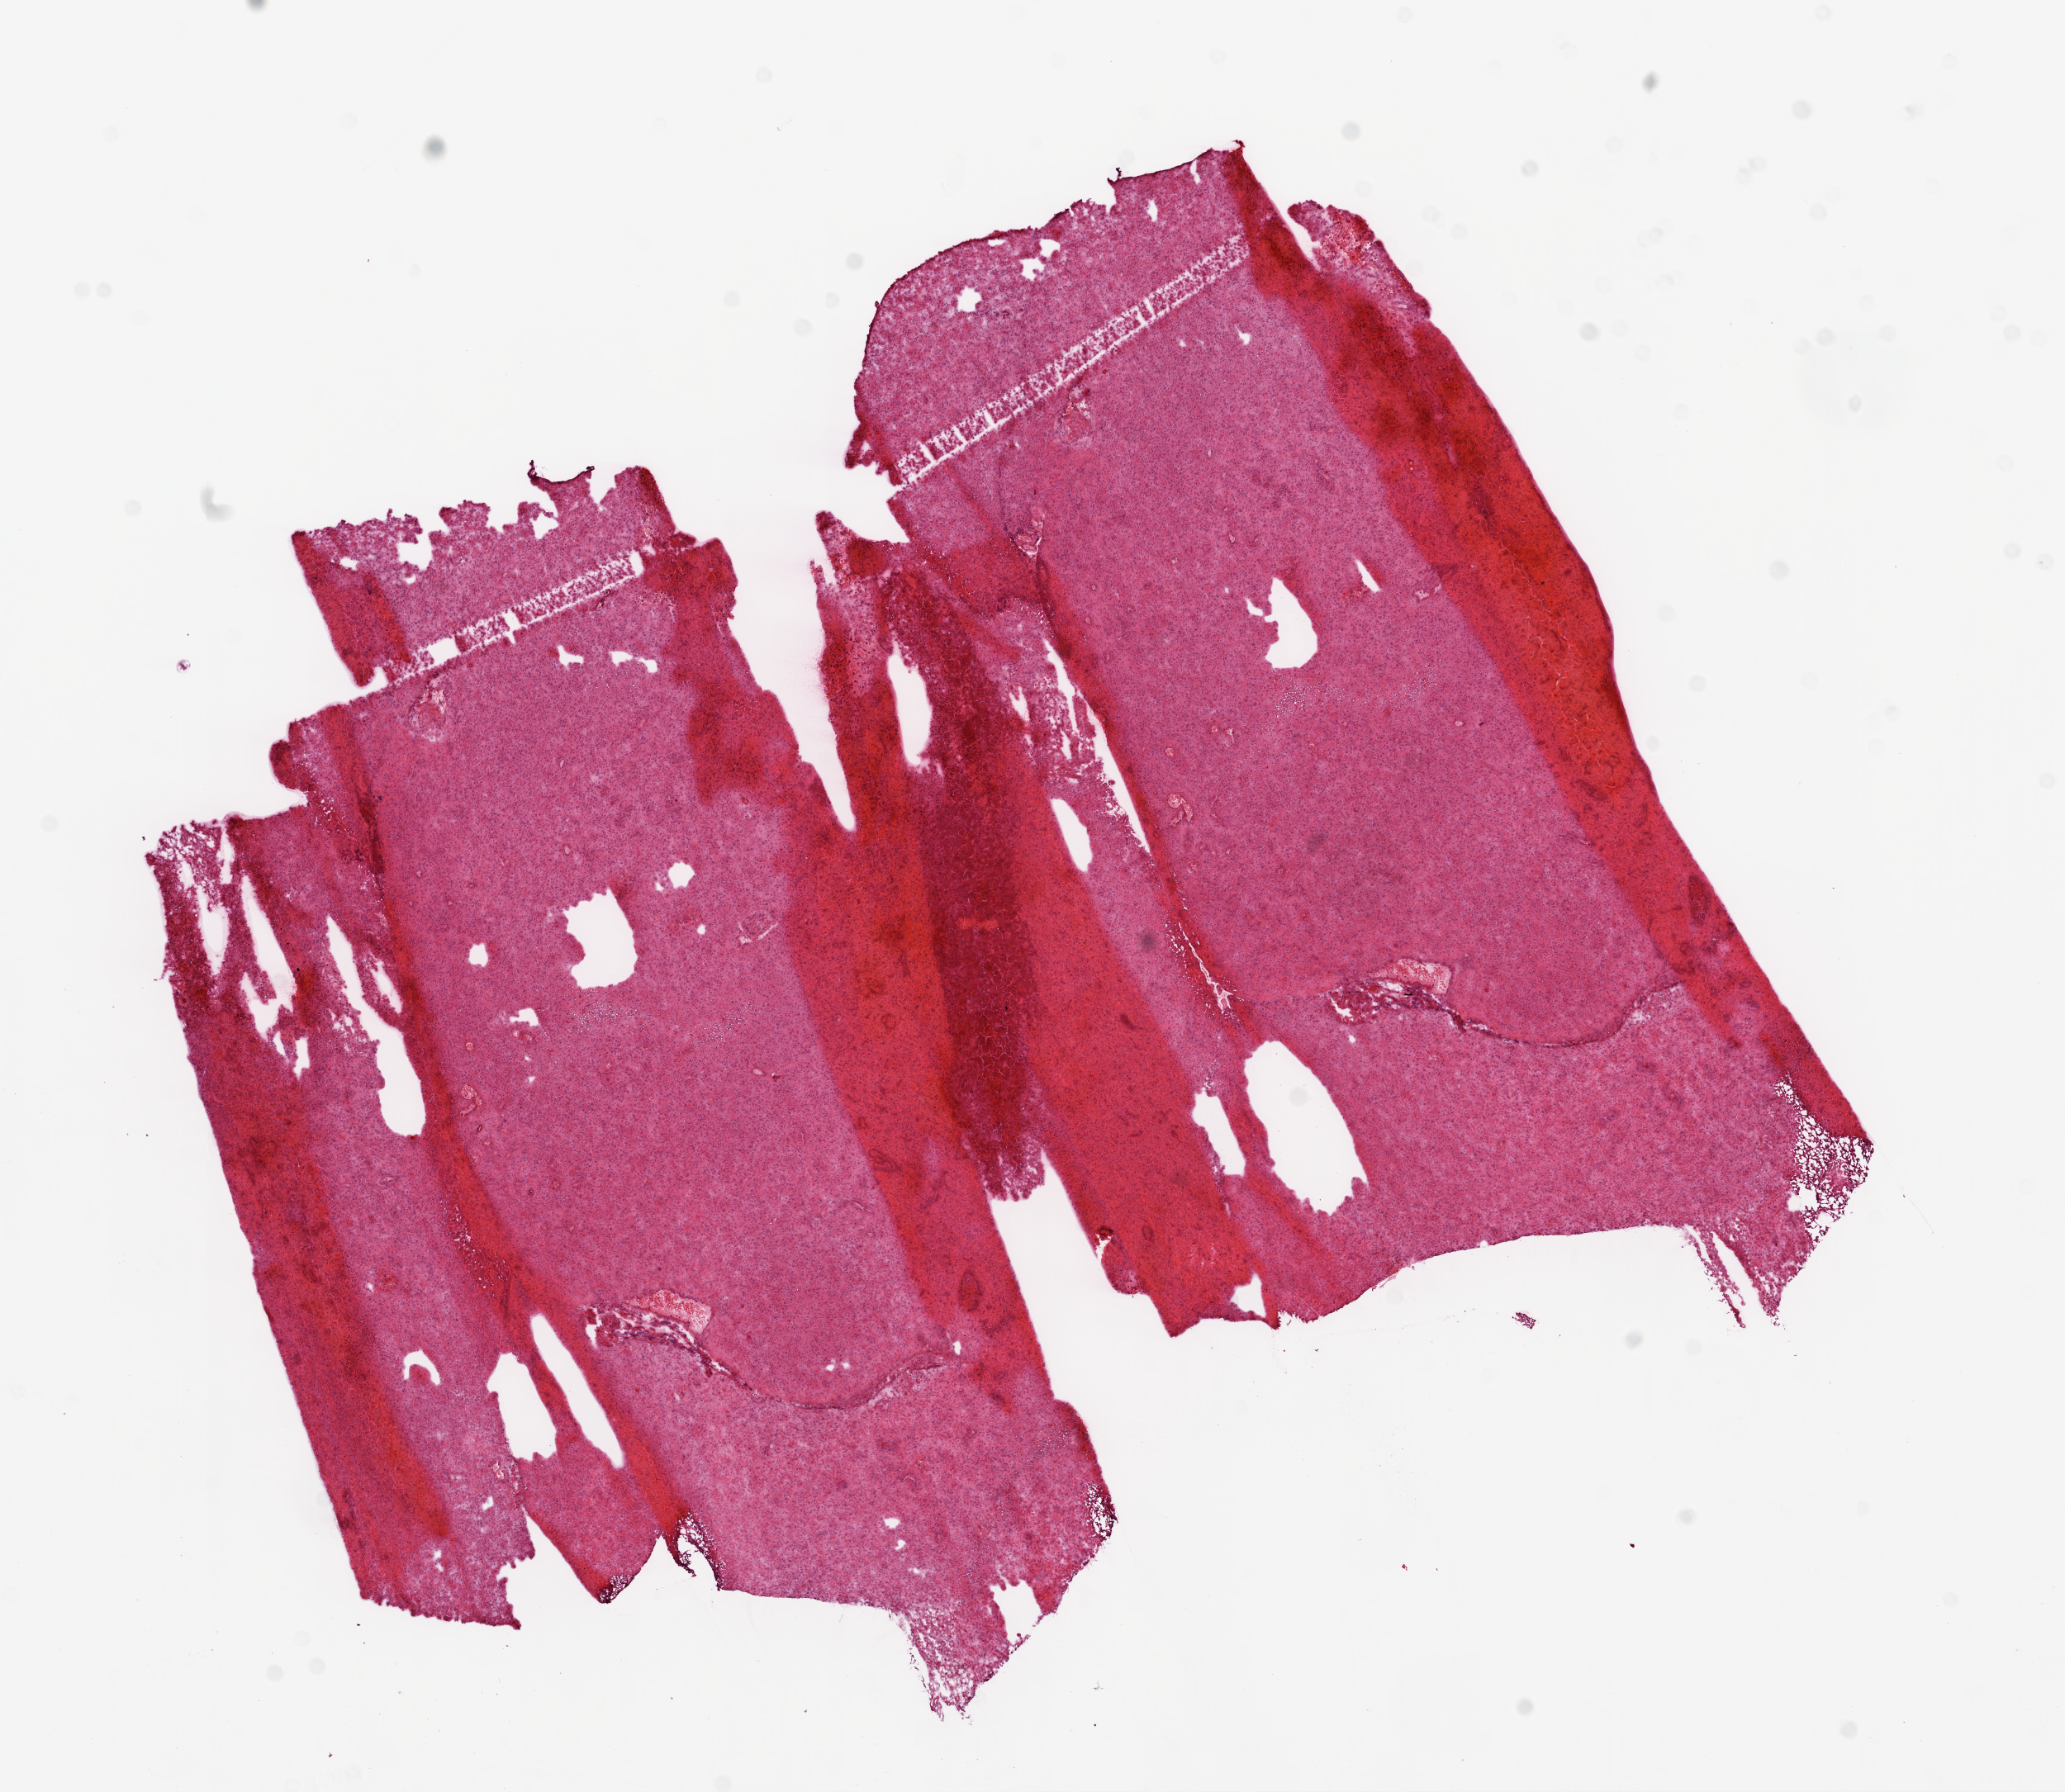
Whole-slide histology image, Hematoxylin and eosin (H&E) stained — whole scanned area (about 10.0 x 8.7 mm) shown as a low-resolution overview, frozen section, primary tumour sample from the brain. Male patient; age at initial diagnosis 72 years. Slide review estimates, as recorded: tumour cells 100%, tumour nuclei 95%, normal cells 0%, stromal cells 0%, necrosis 0%.
* diagnosis: Glioblastoma